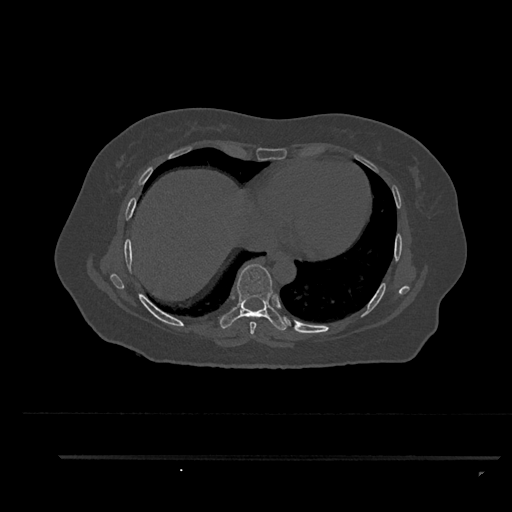
CT including the spine, one axial slice. Position 471 of 797 along the scan axis. Reconstruction kernel Br40s/3. 120 kVp. Bone window (W 1800 / L 400 HU). 0.5 mm slice thickness. 512 × 512 image matrix. Patient: female, 44 years. Case-level facts recorded for this patient, not image findings: primary cancer: renal.
Annotated regions visible in this slice (semi-automatic segmentation, software-assisted and operator-edited):
- T7 vertebra: bounding box (x1, y1, x2, y2) in pixels: (250, 322, 257, 335)
- T8 vertebra: (218, 264, 288, 331)